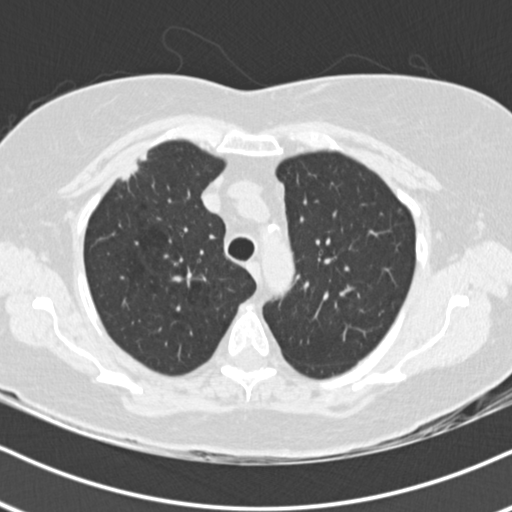
Axial slice from a low-dose chest CT screening exam, baseline screening round, lung window (W 1500 / L -600 HU), 2 mm slice thickness, standard (soft-tissue) reconstruction kernel (B30f). Female, age 74 years at enrolment. Former smoker at enrolment.
Expert-annotated lung lesion, bounding box <101,141,164,196> (left, top, right, bottom; pixels). Reader record for this screening exam (exam-level; its link to the box is not recorded): non-calcified nodule or mass ≥4 mm, right upper lobe, 16 × 10 mm, poorly defined margins, soft tissue attenuation. Participant outcome: lung cancer diagnosed 33 days after this screen — adenocarcinoma, NOS, right upper lobe, poorly differentiated (G3), stage IIIA (AJCC 6th edition), 24 mm at pathology.